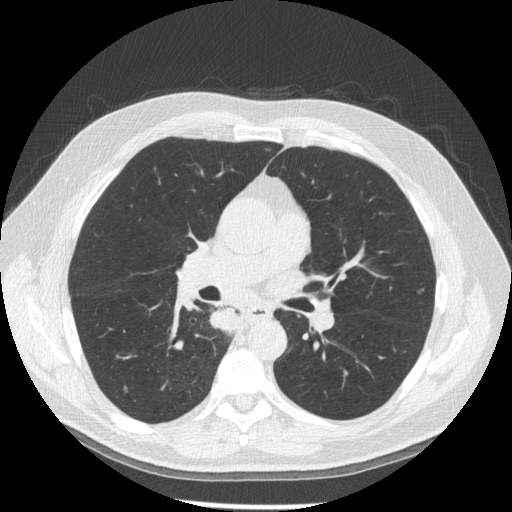
Low-dose screening chest CT, one axial slice. Slice 103 of 181 in the series (ordered by position). 120 kVp. Lung window (W 1500 / L -600 HU). 512 × 512 image matrix, field of view 370 × 370 mm.
Outlined on this slice (outlined manually by an expert reader):
- lesion 1 (tumor, lower lobe of right lung): bounding box [x1, y1, x2, y2] px = [210, 307, 238, 334]